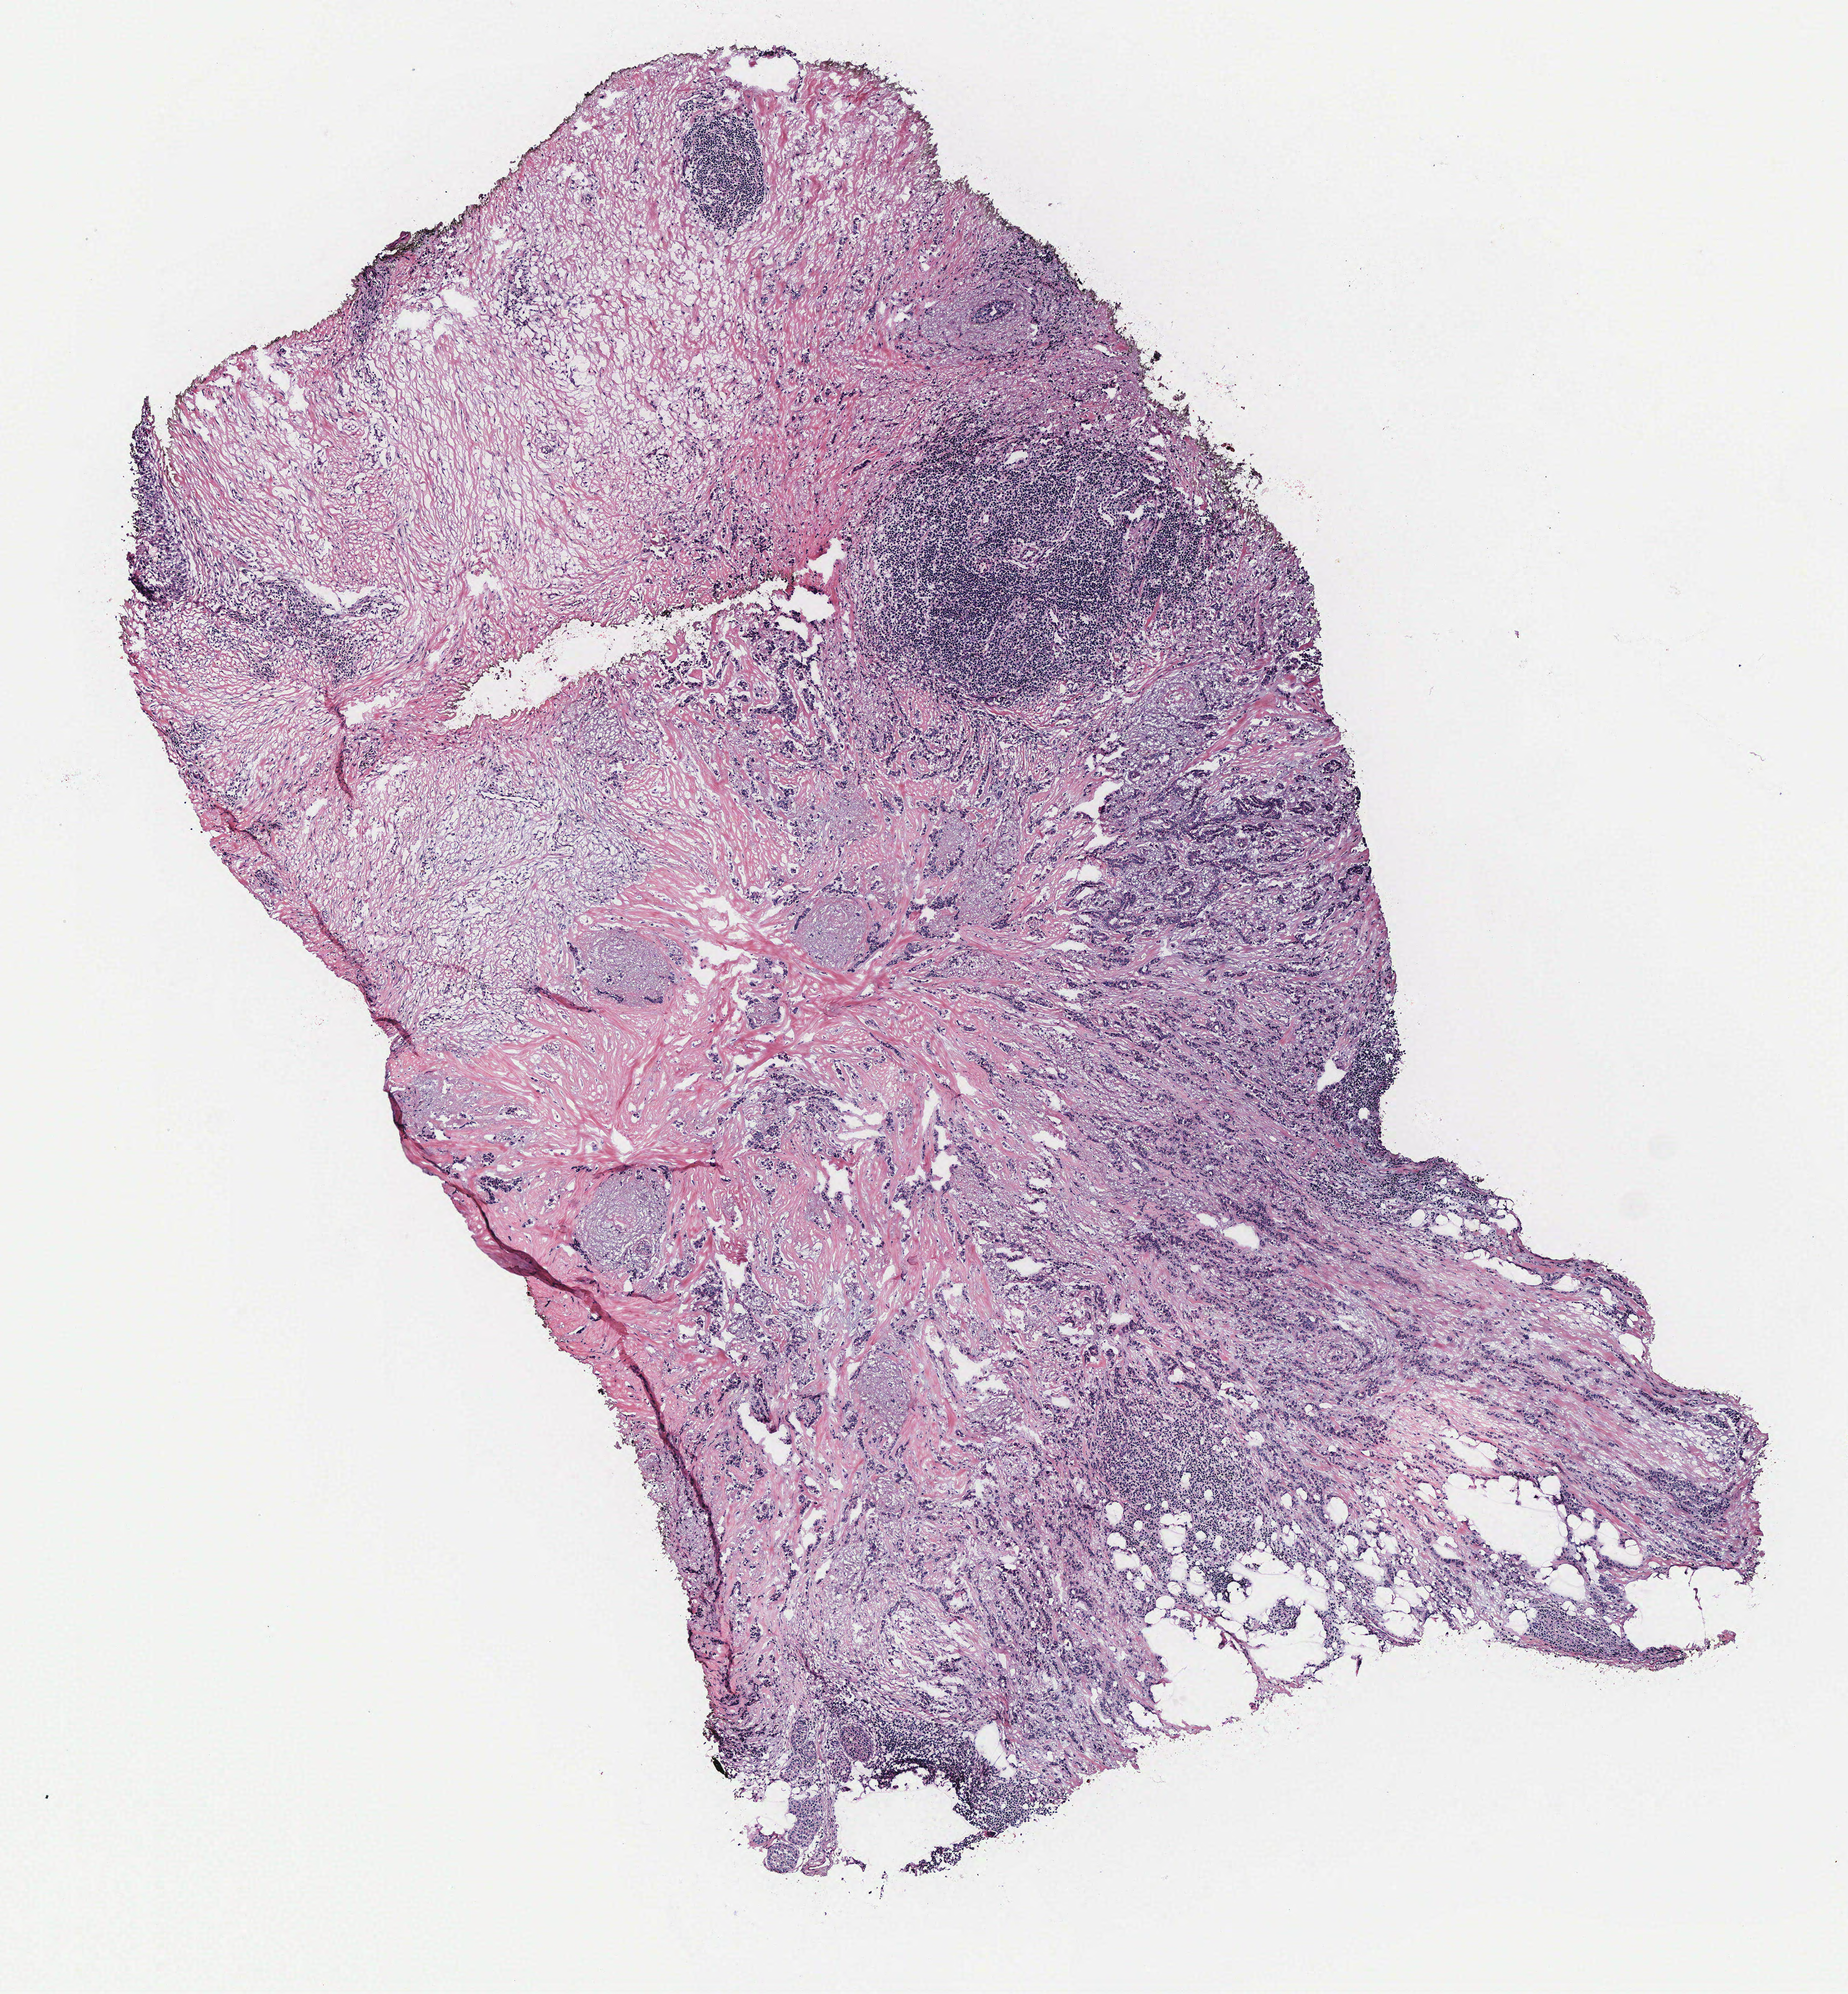
H&E-stained whole-slide image, a low-resolution overview of the entire scanned area, about 5.8 x 6.2 mm (from a 40x scan); breast, tissue type not recorded.
Patient diagnosis (cohort enrolment): breast cancer (breast).